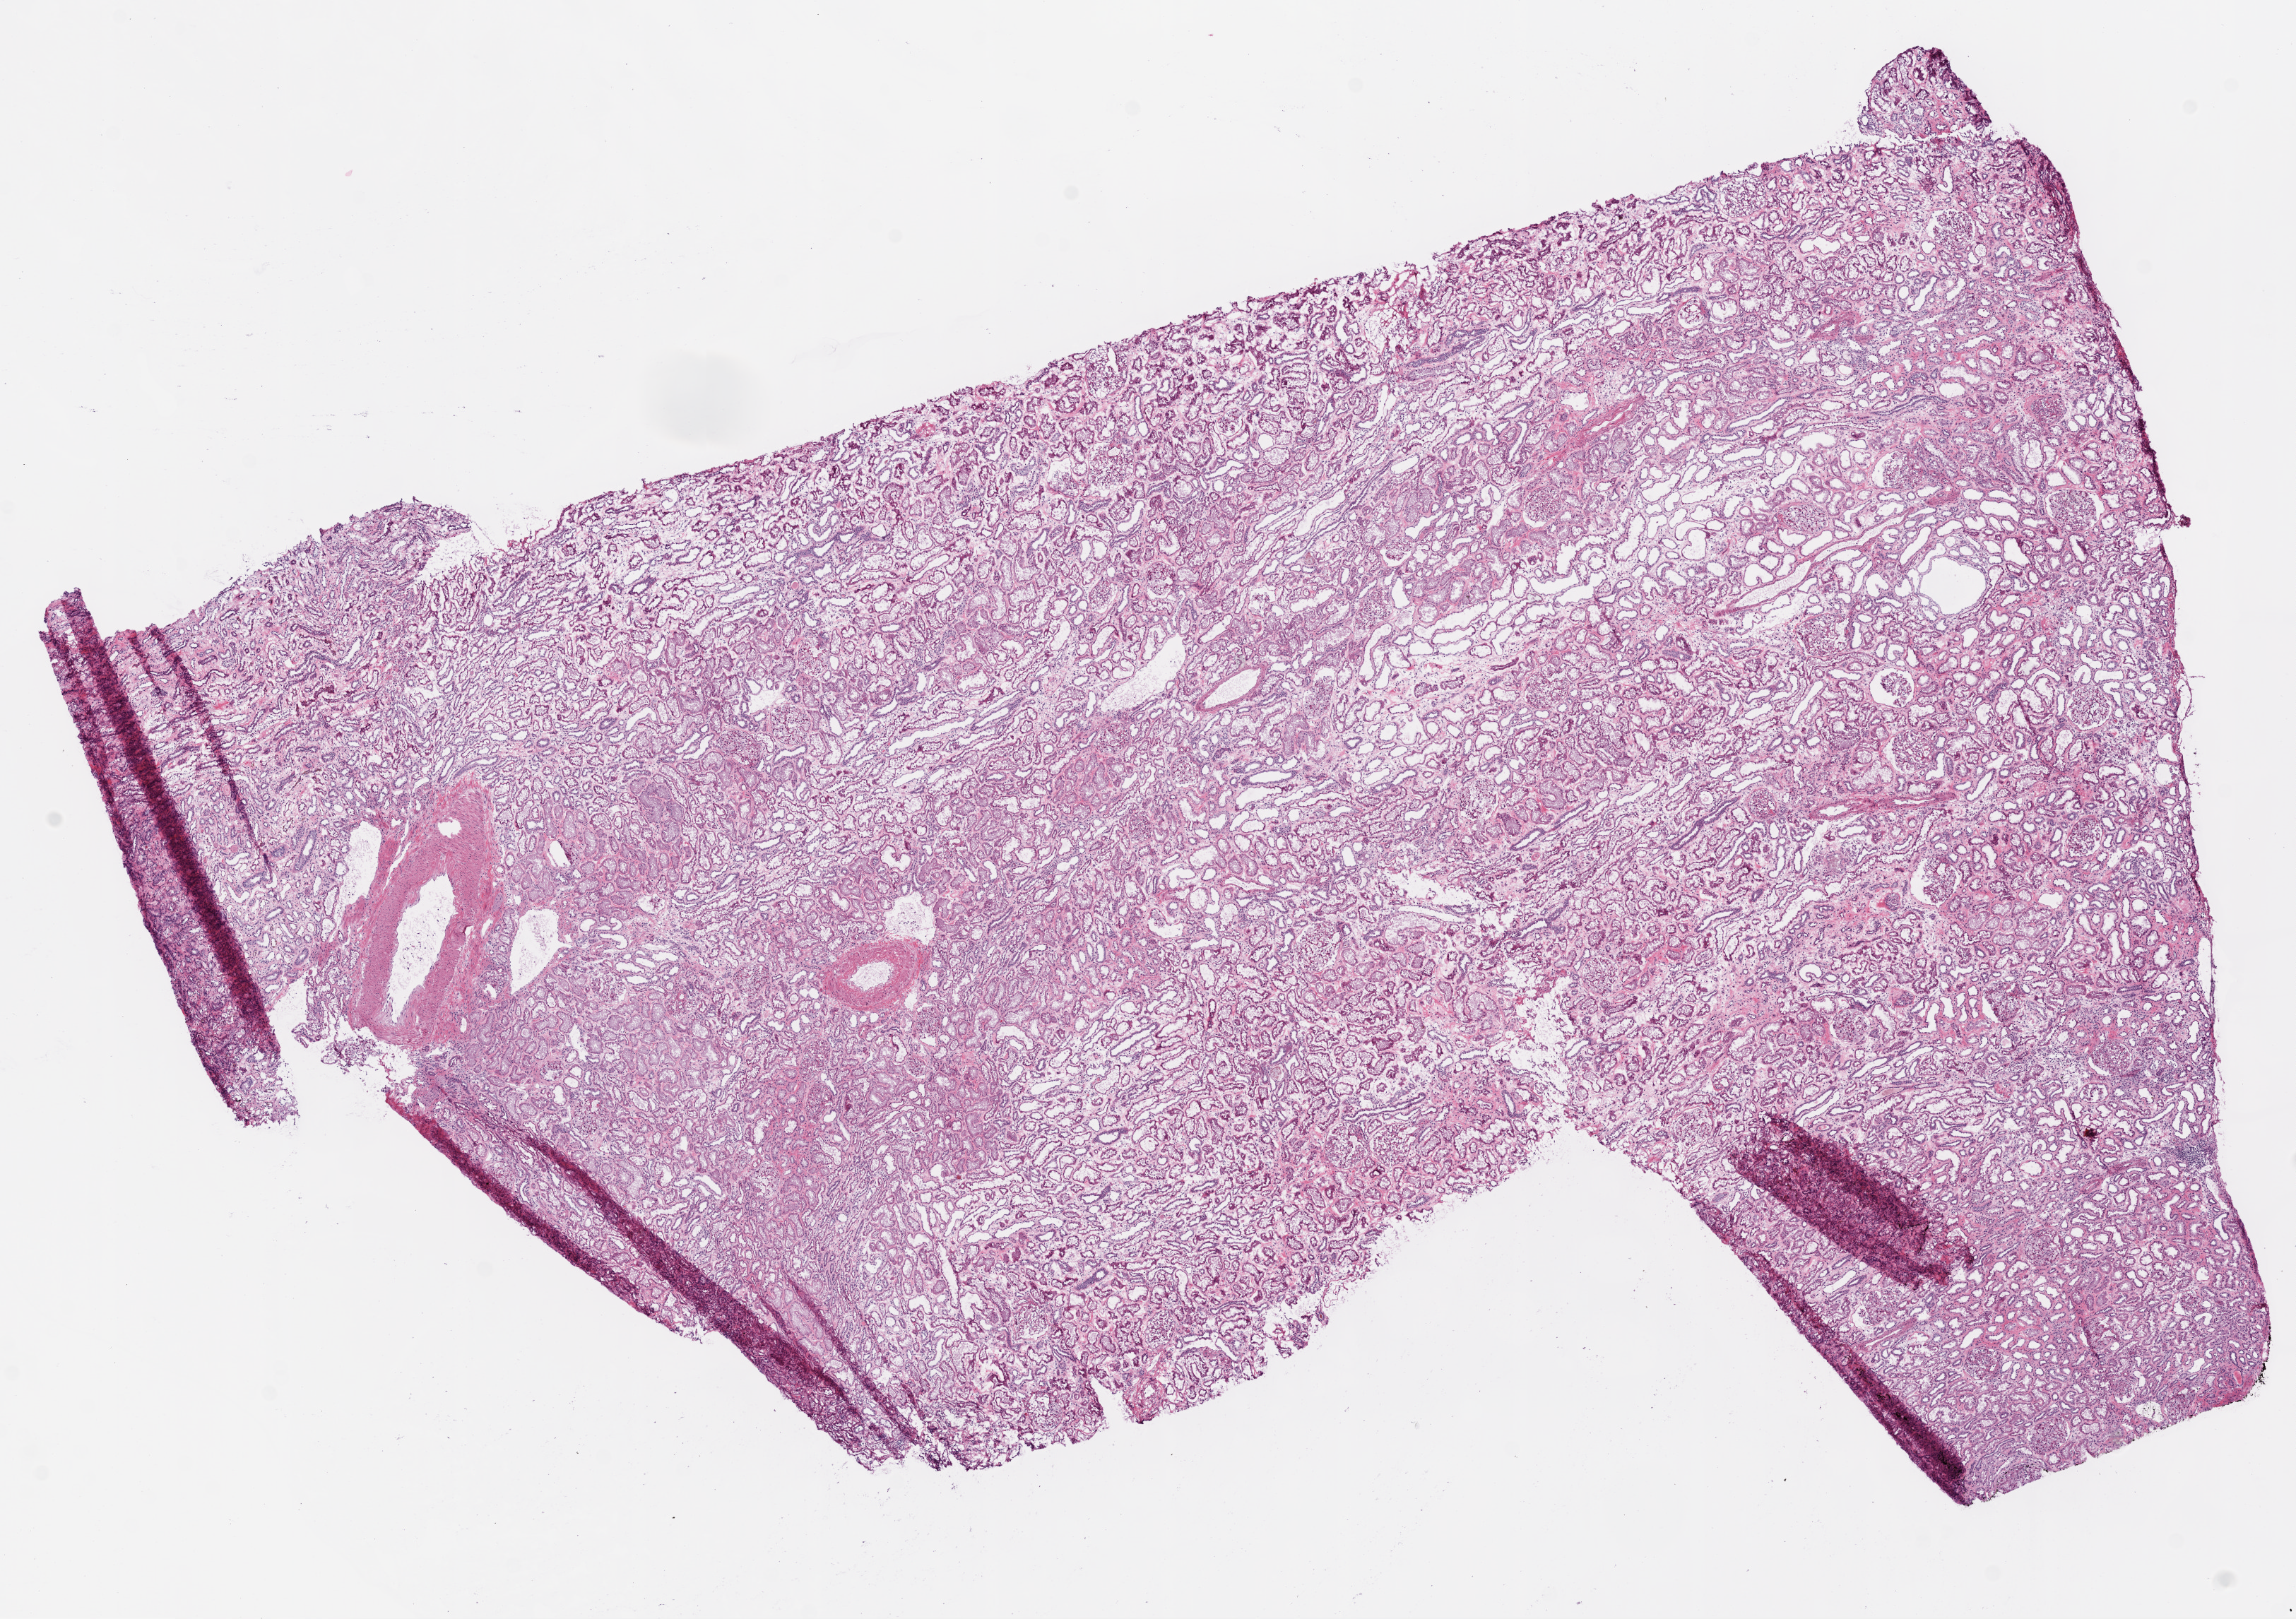
Digitized H&E-stained tissue section (whole slide), whole scanned area (about 13.0 x 9.2 mm, from a 20x scan) shown as a low-resolution overview; frozen section; solid tissue normal (non-tumour tissue) sample from the kidney. Female, age 52 years at initial diagnosis.
- this section: solid tissue normal sample (biorepository sample class)
- patient diagnosis: Clear cell adenocarcinoma, NOS